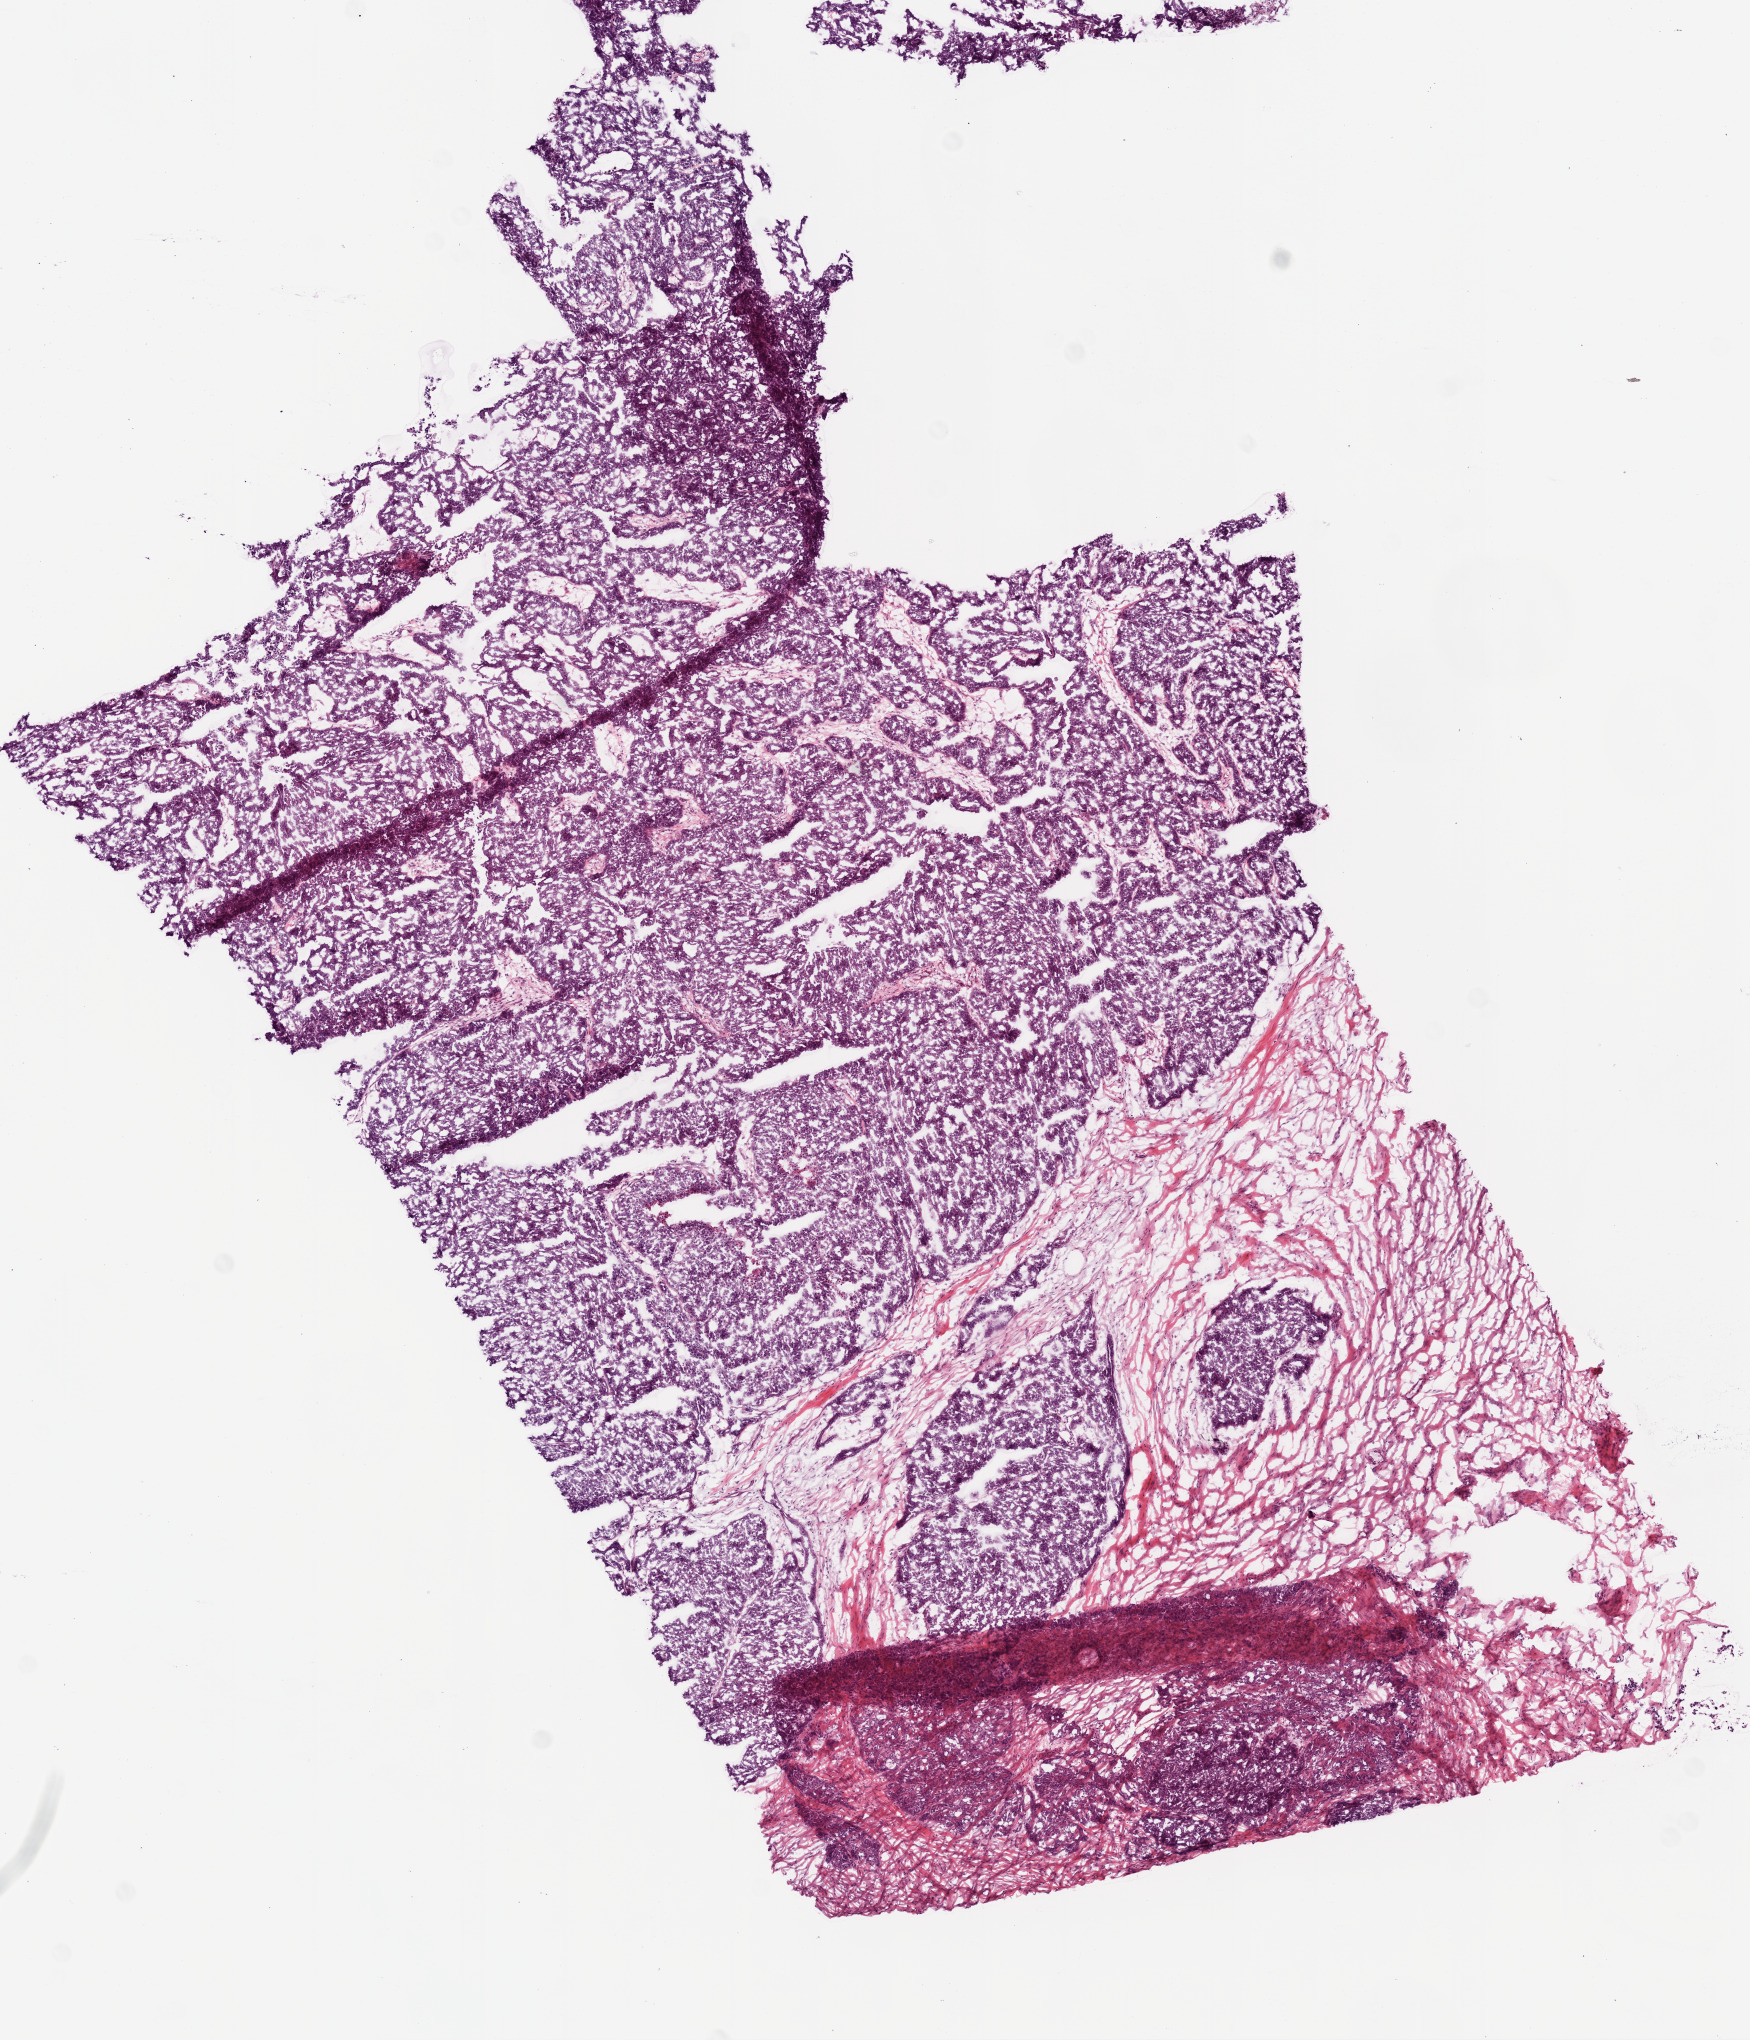
Digitized Hematoxylin and eosin (H&E) stained tissue section (whole slide) — whole scanned area (about 7.0 x 8.2 mm, acquisition: 20x scan) shown as a low-resolution overview. Frozen section from the bottom of the tissue portion. Sample: primary tumour, ovary. Female, age 50 years at initial diagnosis. Histologic grade: G3 (poorly differentiated). Pathologist review of this section (percent, as recorded): tumour cells 75%, tumour nuclei 90%, normal cells 0%, stromal cells 25%, necrosis 0%.
FIGO stage: IIIC. Pathologic diagnosis: Serous cystadenocarcinoma, NOS.